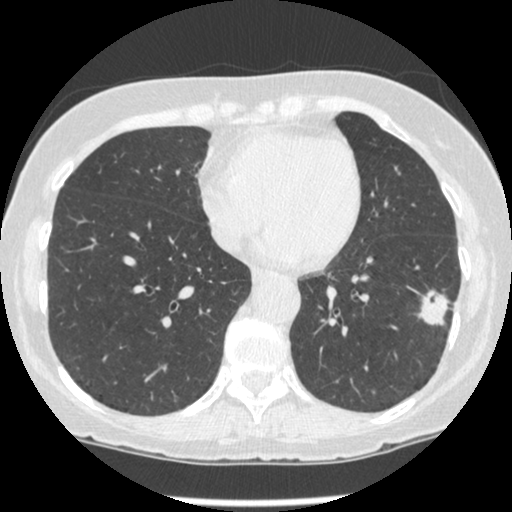
Low-dose screening chest CT, one axial slice. Slice 91 of 247 in the series (ordered by position). 120 kVp. Lung window (W 1500 / L -600 HU). 1.25 mm slice thickness. 512 × 512 image matrix.
Structures marked on this image (outlined manually by an expert reader):
- lesion 1 (tumor, lower lobe of left lung): bounding box <419,290,450,325> (left, top, right, bottom; pixels)